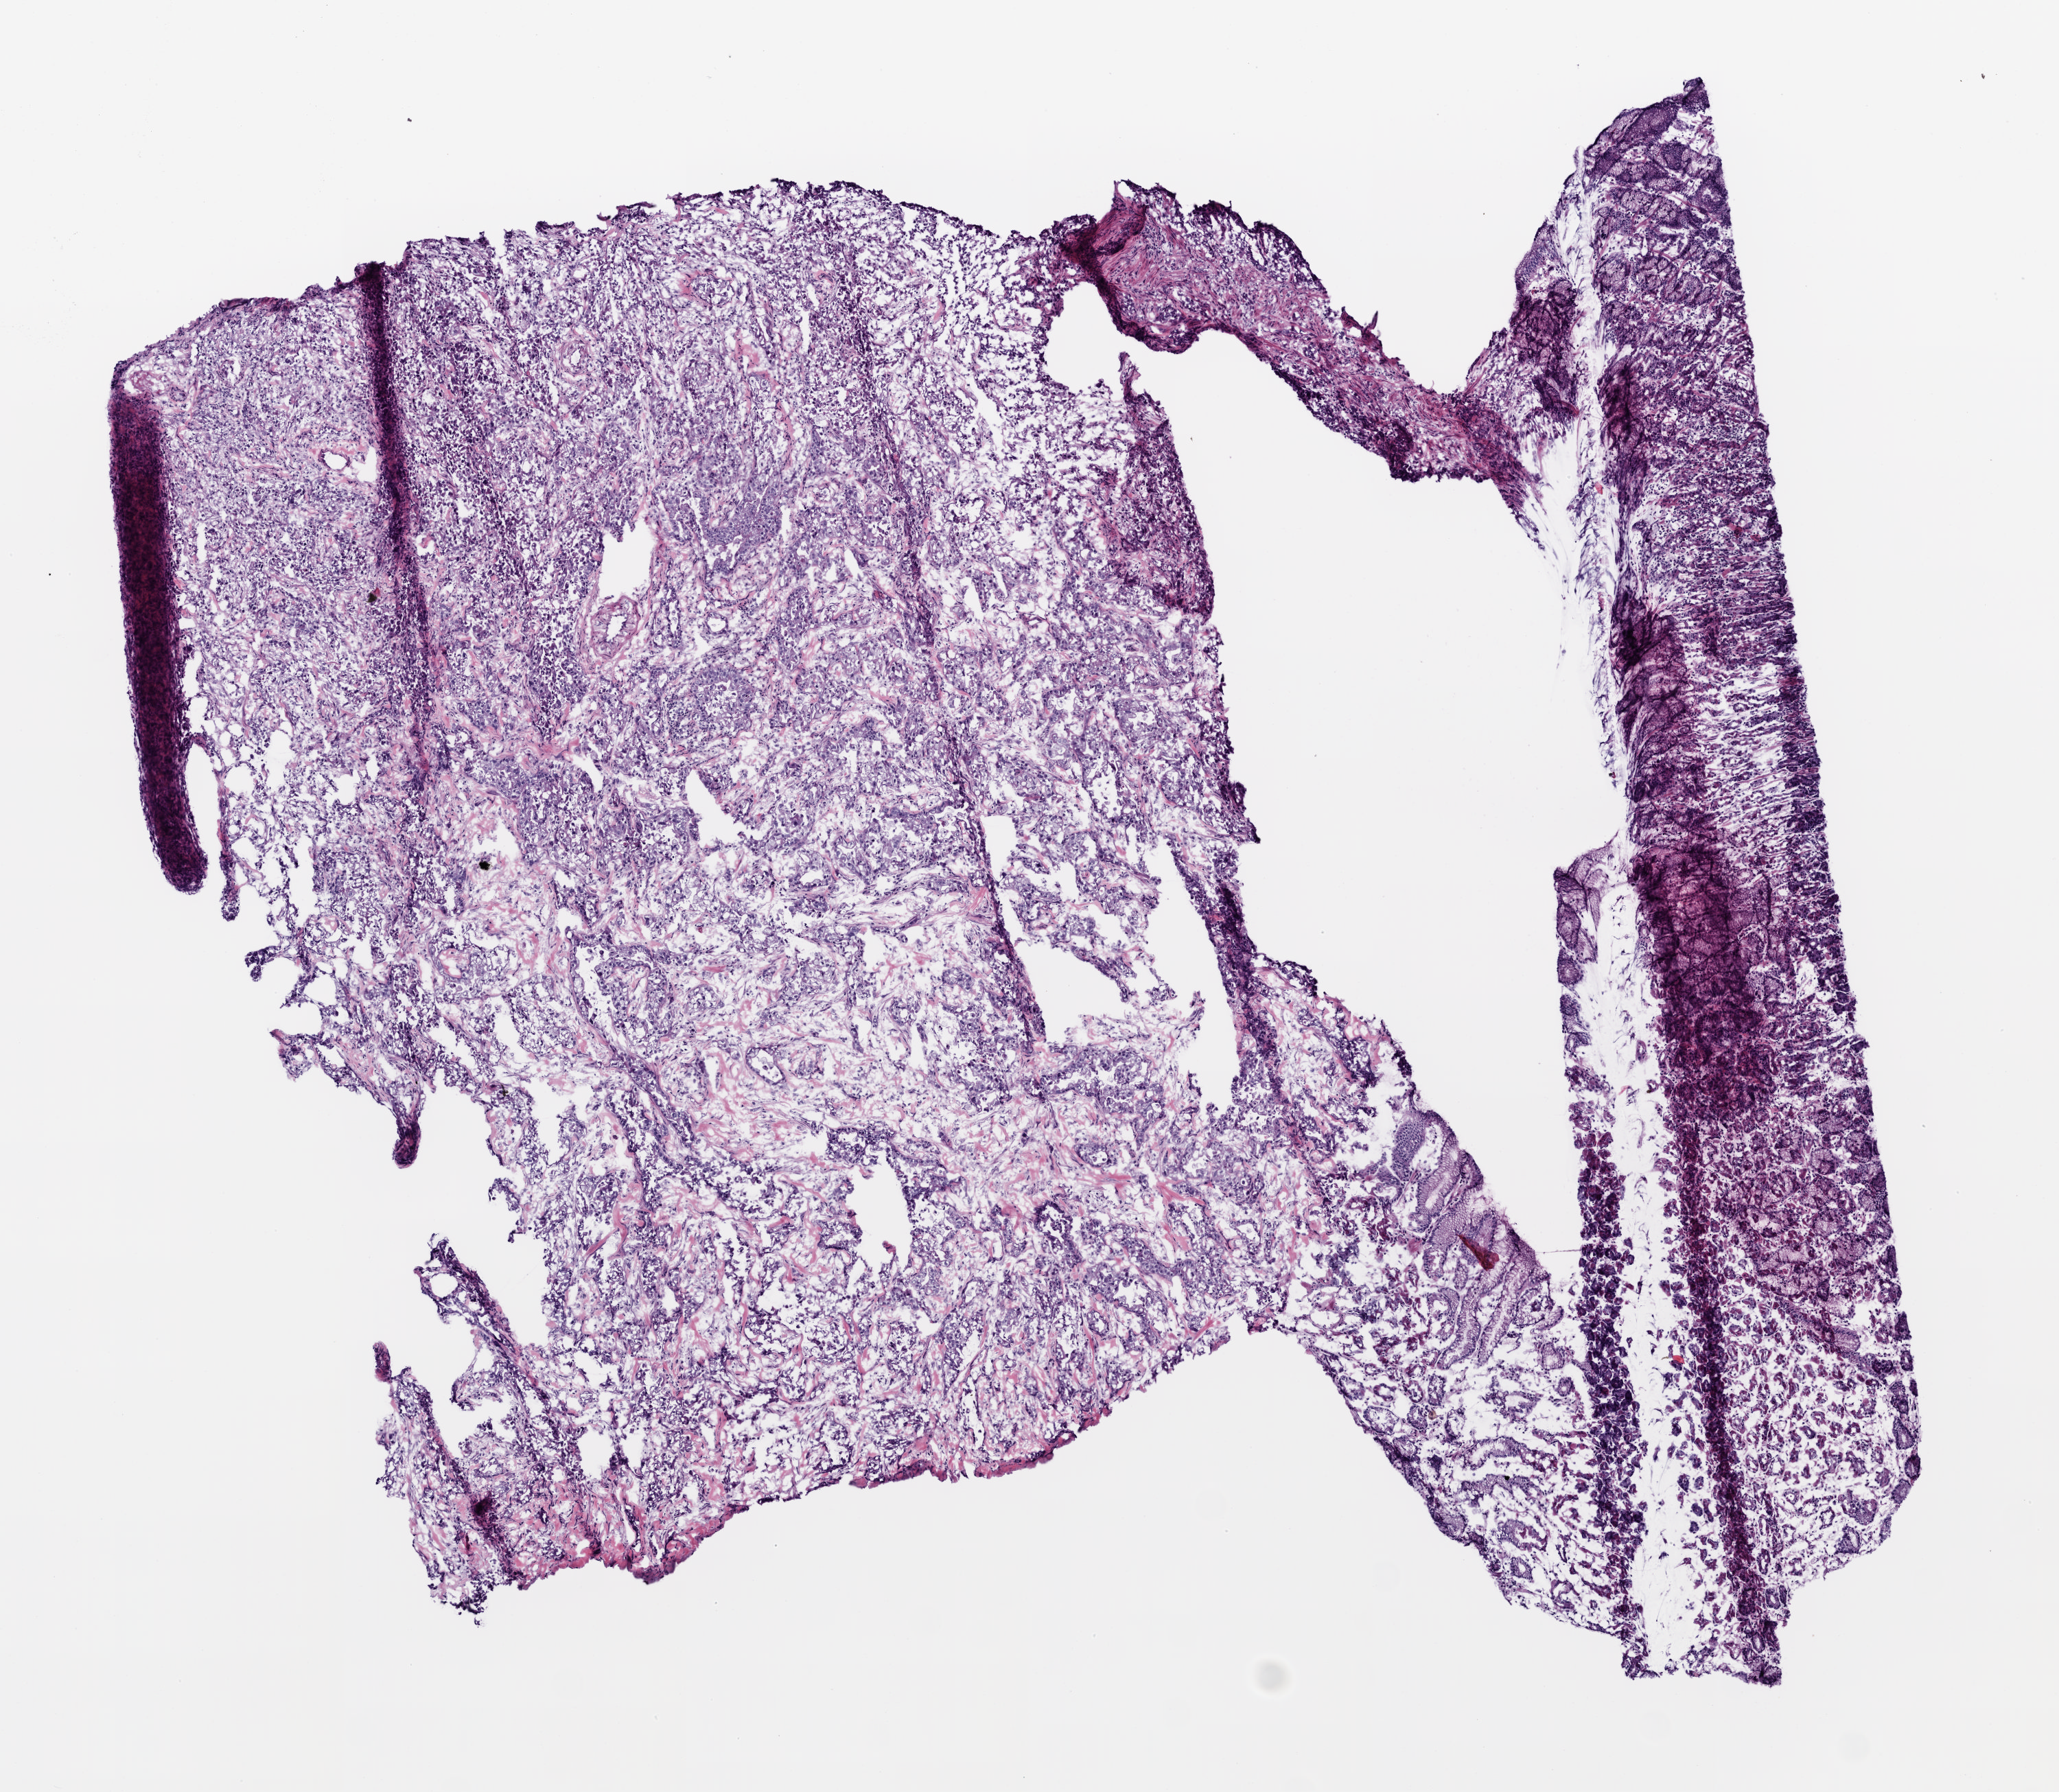
Whole-slide histology image, Hematoxylin and eosin (H&E) stained, a low-resolution overview of the entire scanned area, about 6.0 x 5.2 mm (slide scanned at 20x); frozen section; primary tumour sample from the stomach. Female, age 75 years at initial diagnosis. Composition of this section per pathologist review: tumour cells 78%, tumour nuclei 77%.
Histologic diagnosis: Adenocarcinoma, NOS (cardia, NOS).